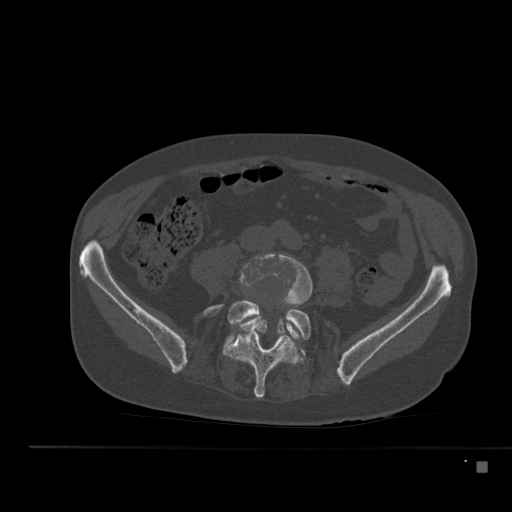
CT including the spine, one axial slice; position 131 of 517 along the scan axis; bone window (W 1800 / L 400 HU); 1.5 mm slice thickness; 512 × 512 image matrix. Male patient, age 70 years. From the clinical record (not read from this slice): primary cancer: renal; vertebrae with lytic lesions (as recorded): T4, T6, T10, T12, L3, L4, L5.
Structures marked on this image (semi-automatic segmentation, software-assisted and operator-edited):
- L4 vertebra: bounding box [x1, y1, x2, y2] px = [239, 253, 313, 340]
- L5 vertebra: [204, 300, 311, 398]